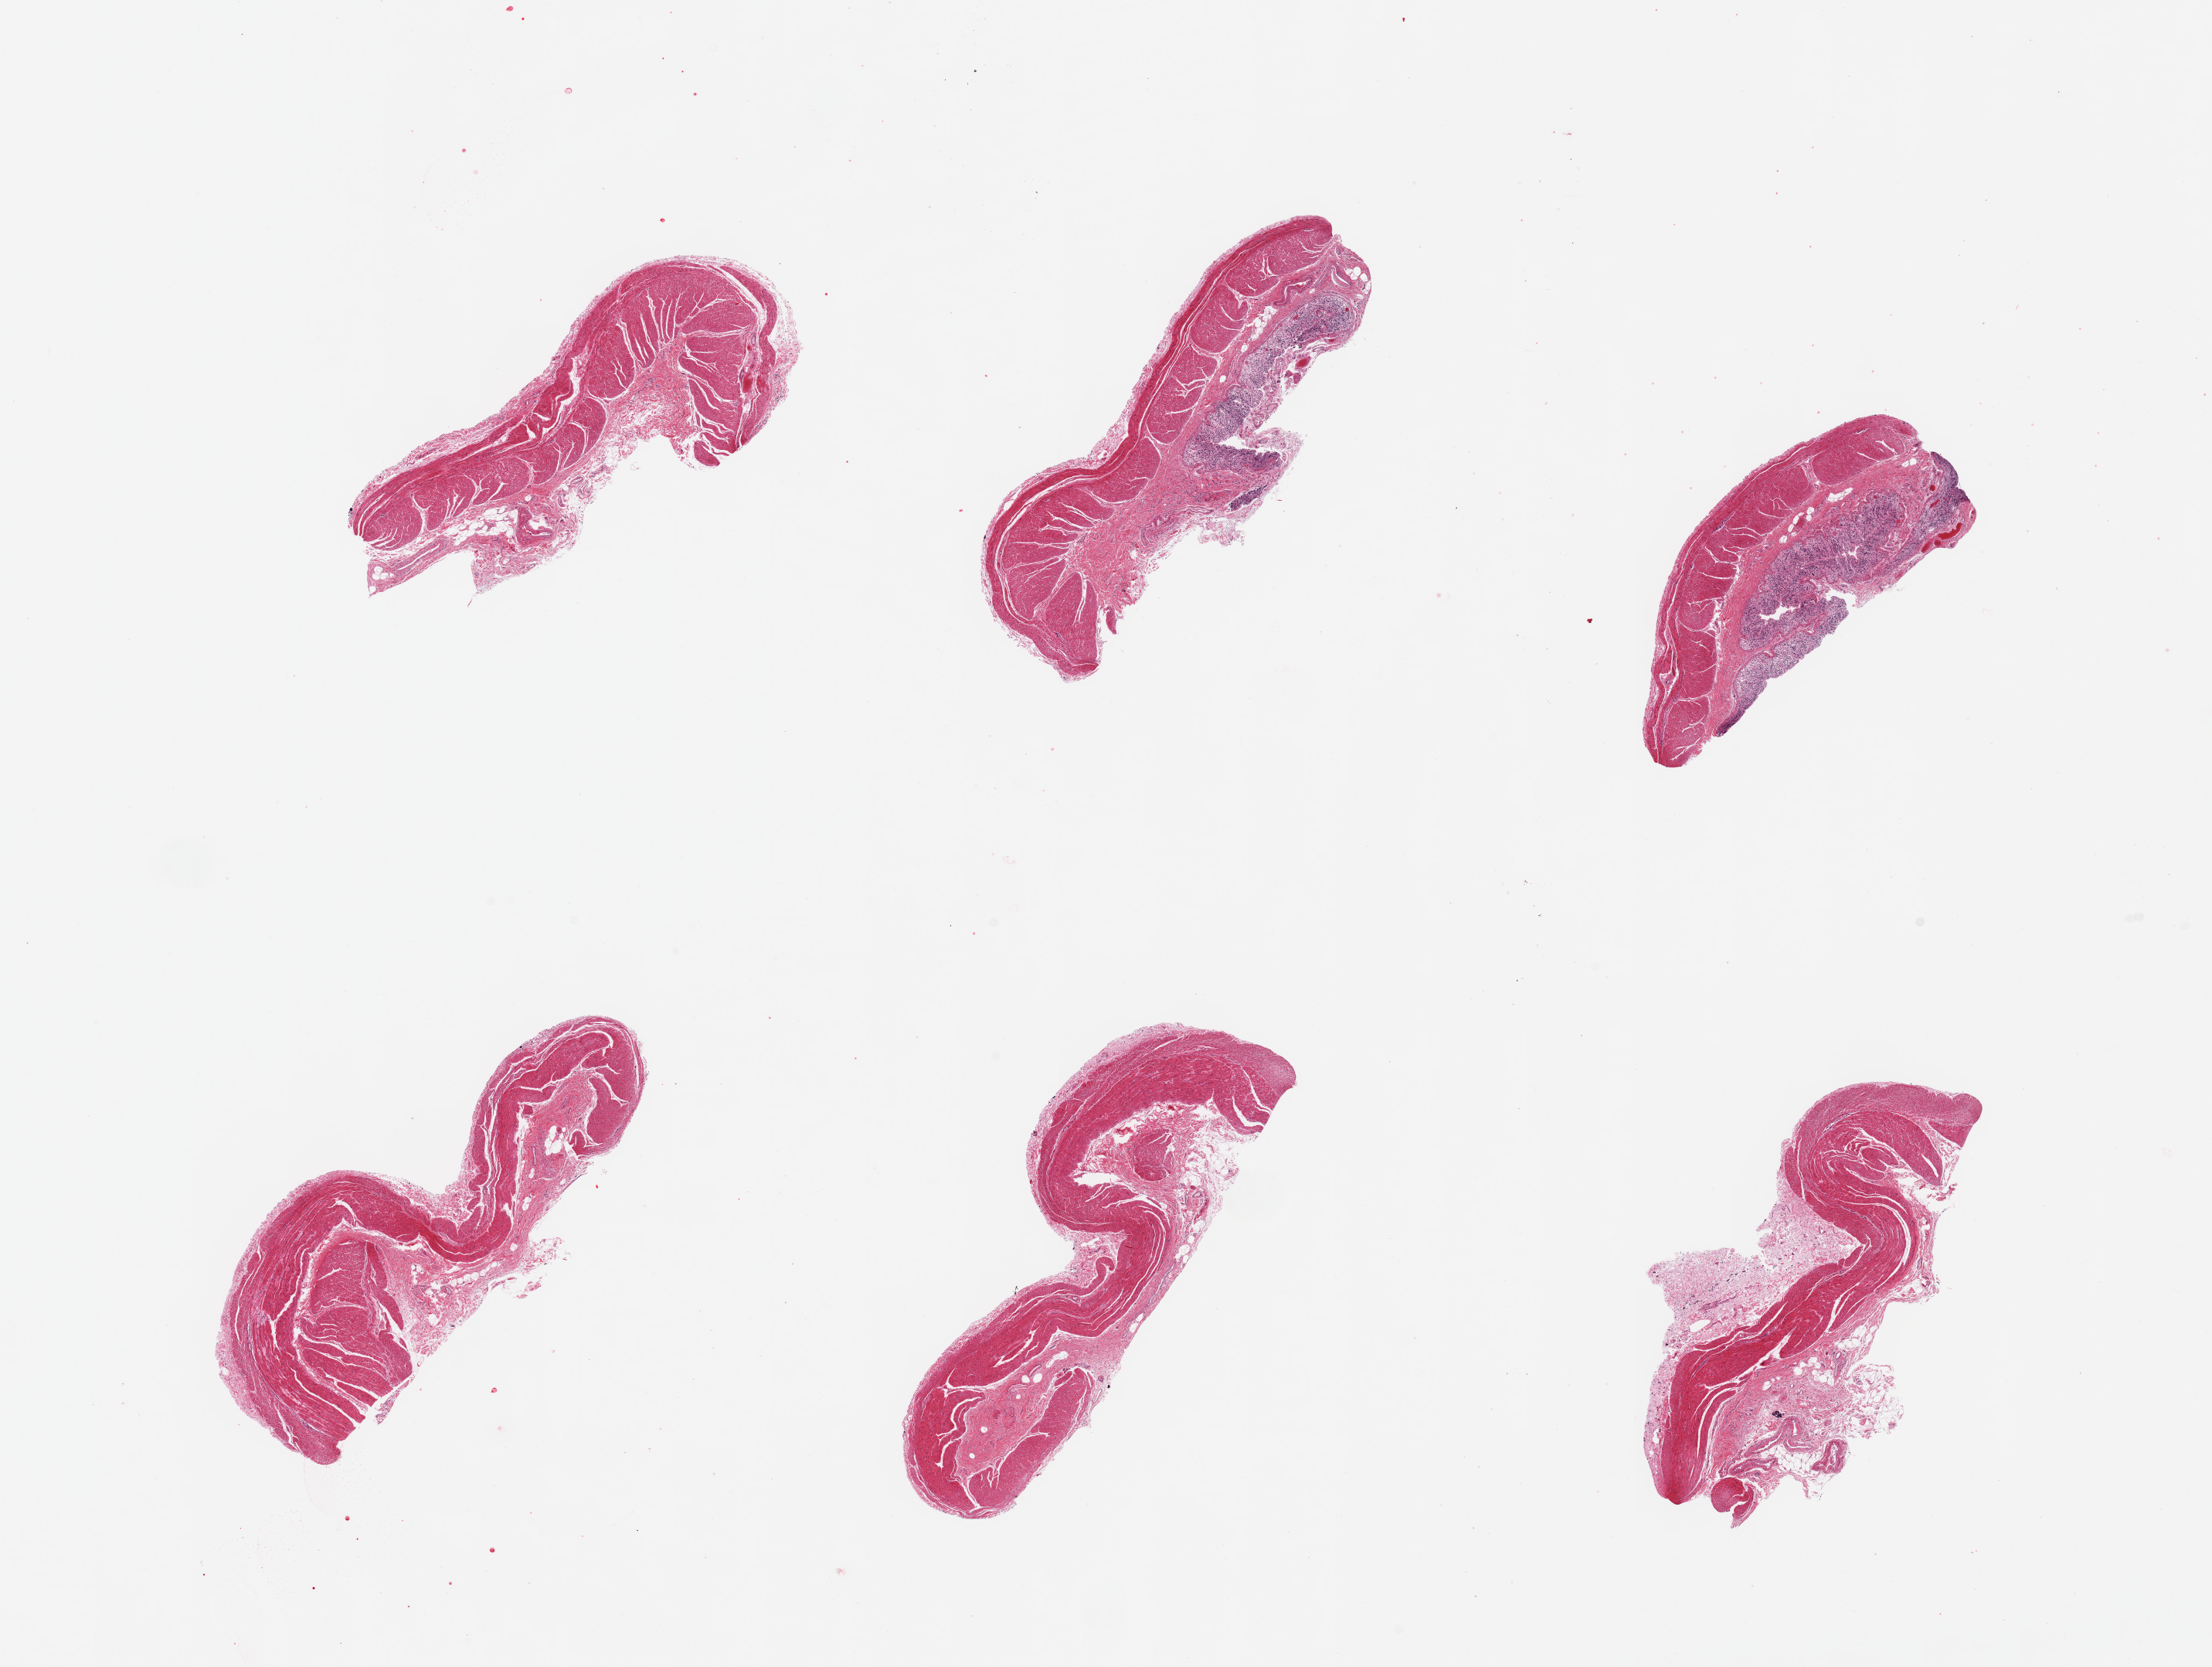
Digitized haematoxylin and eosin-stained section — whole scanned area (about 22.6 x 17.1 mm, from a 20x scan) shown as a low-resolution overview, PAXgene-fixed, paraffin-embedded tissue, target tissue: transverse colon, donor tissue sample. Donor sex: female.
Reviewer comment on this tissue sample: 6 pieces; 2 have autolyzed mucosa and intact muscularis; 4 have only muscularis; could be used to compare with muscularis of sigmoid.